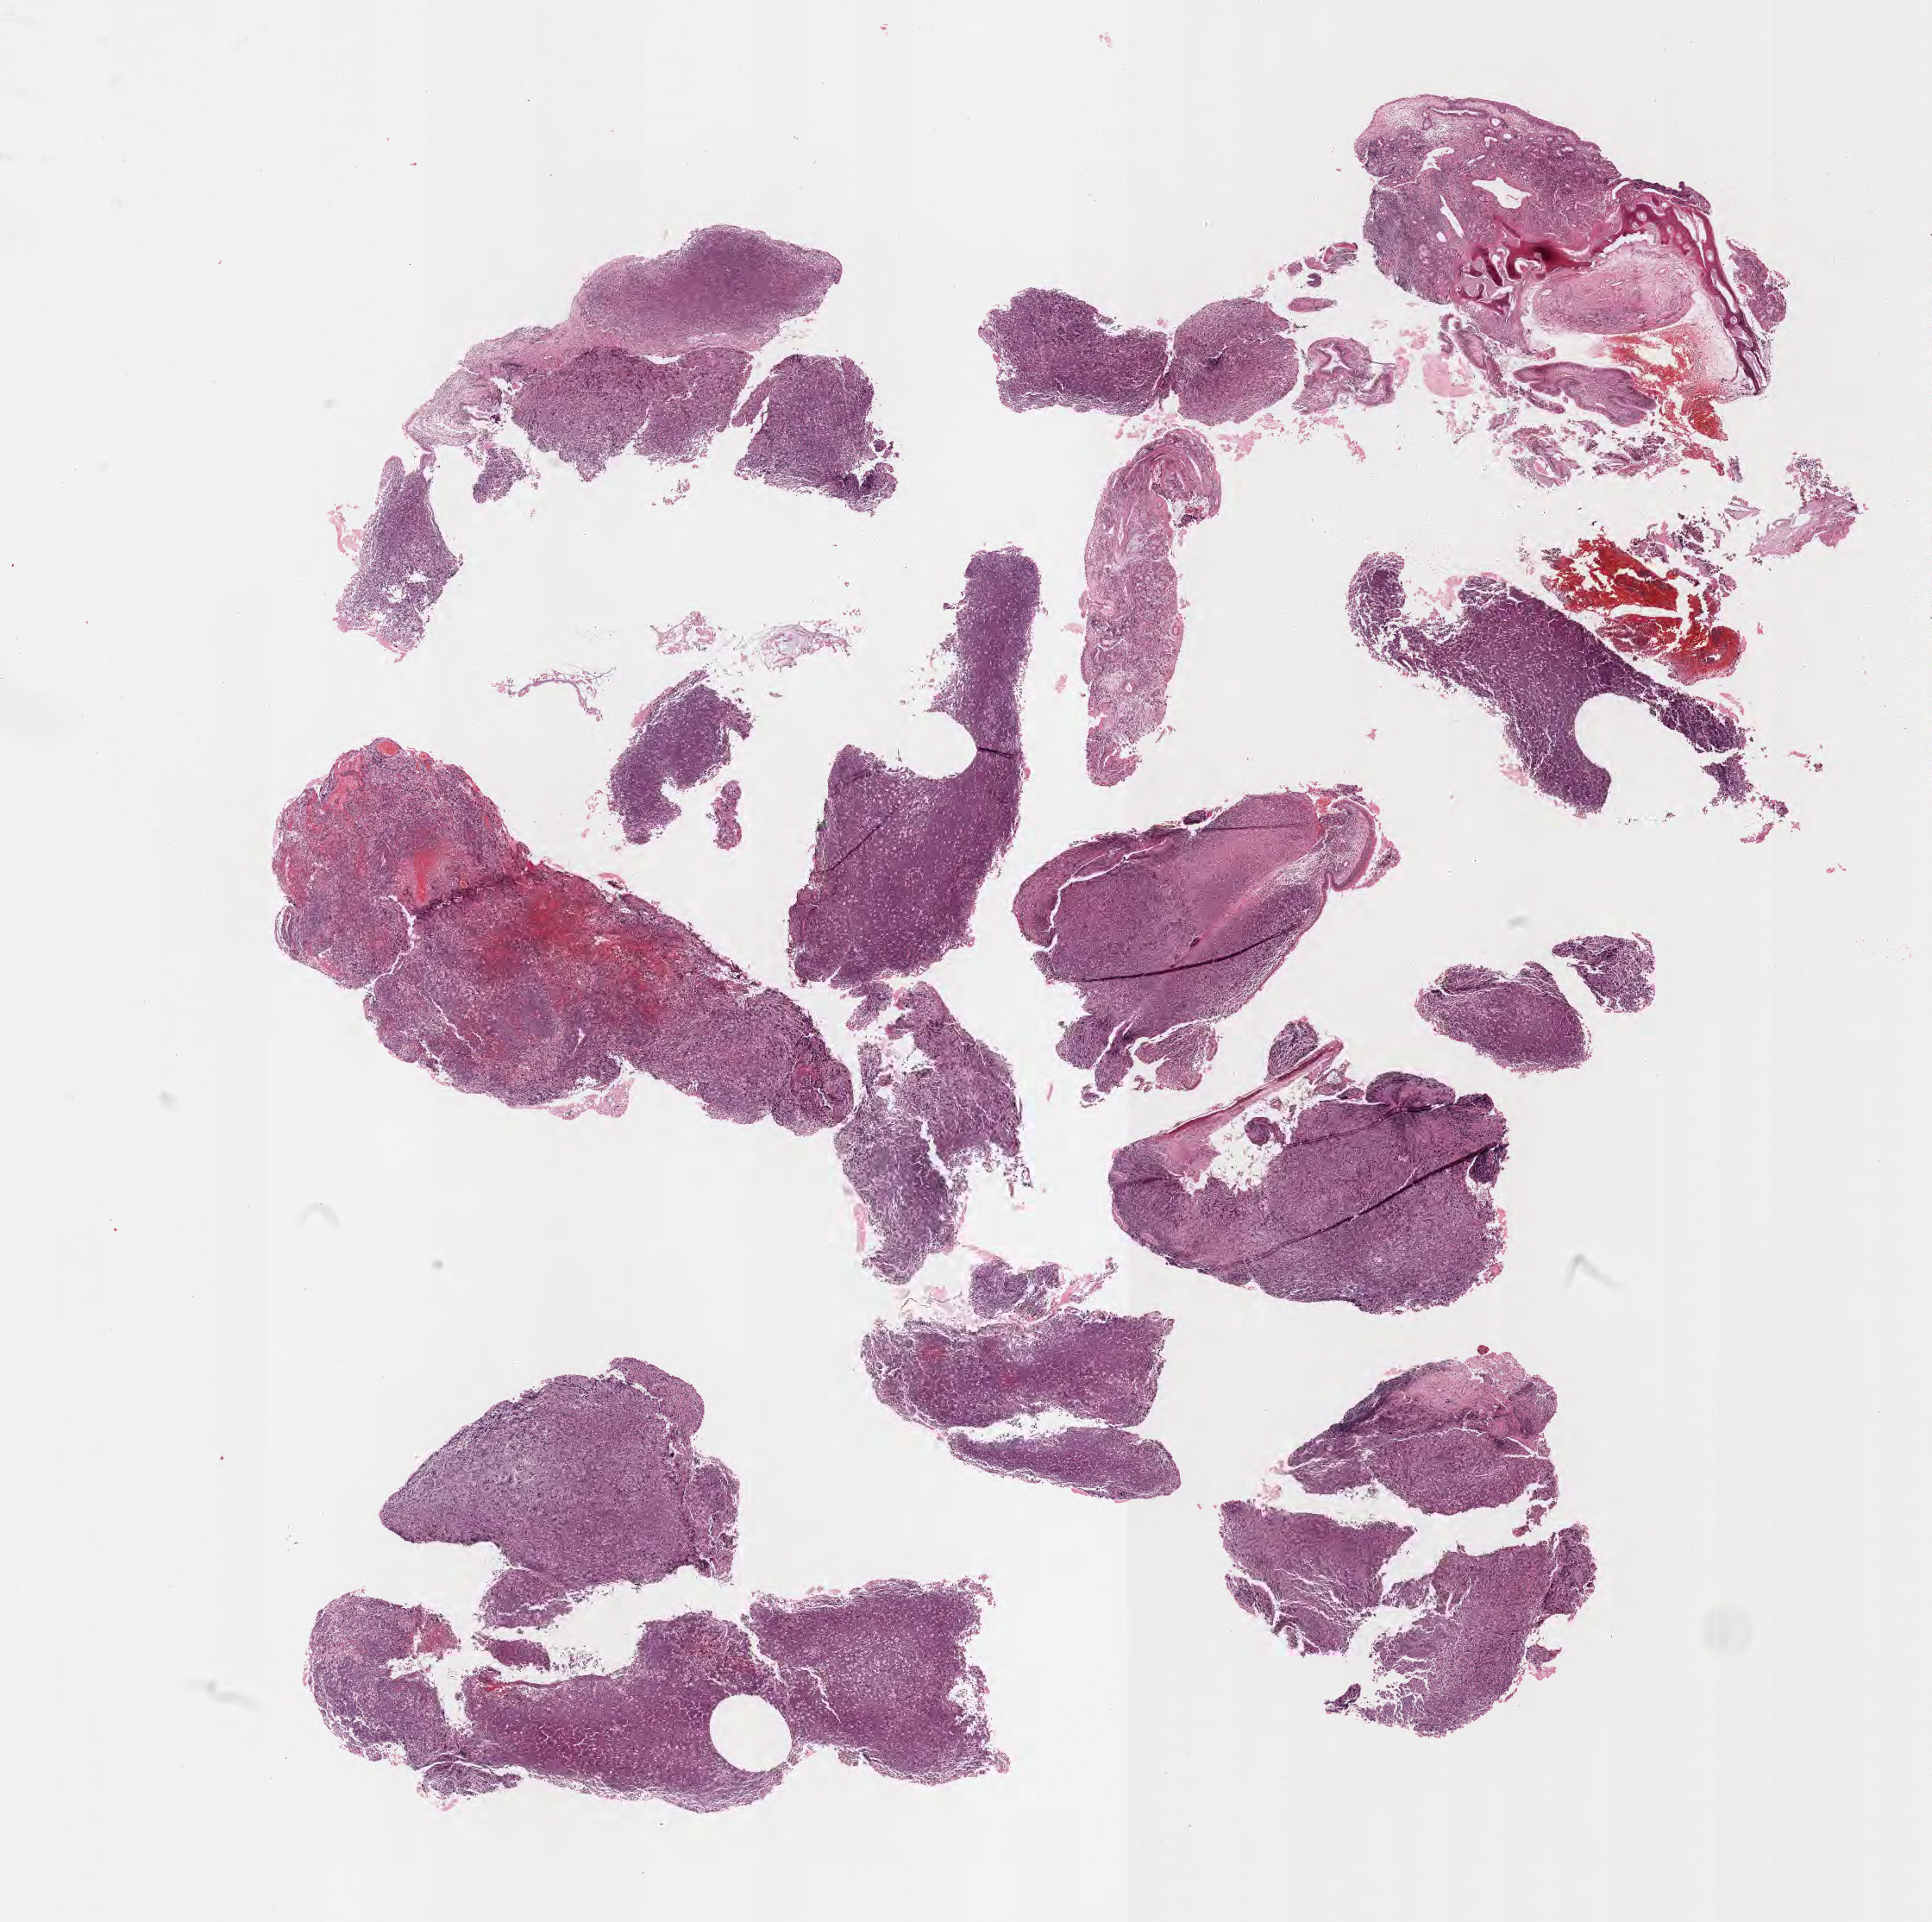
Digitized H&E-stained section, shown as a low-resolution overview of the whole scanned area (about 18.1 x 18.0 mm); FFPE section; specimen: primary tumor. Patient male; aged 38. Composition of this section per pathologist review: tumor cells 80%, tumor nuclei 90%, stromal cells 10%, necrosis 10%, normal cells 0%. Inflammatory infiltration, as recorded: lymphocyte infiltration 50%, monocyte infiltration 25%, neutrophil infiltration 5%.
Section: top of the tissue portion. Ann Arbor stage (patient): Stage I. Histologic diagnosis: Burkitt lymphoma, NOS.